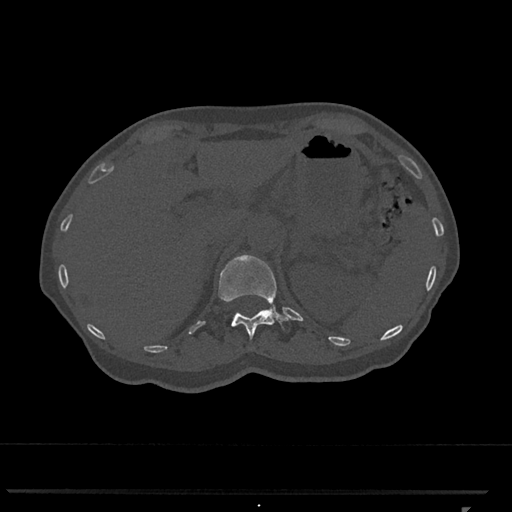
CT including the spine, one axial slice. Position 455 of 793 along the scan axis. Reconstruction kernel Br40s/3. 120 kVp. Bone window (W 1800 / L 400 HU). 512 × 512 image matrix. Female patient, age 62 years. Case-level facts recorded for this patient, not image findings: primary cancer: renal.
Outlined on this slice (semi-automatically segmented with operator editing):
- T12 vertebra: bounding box [x1, y1, x2, y2] px = [218, 255, 290, 340]